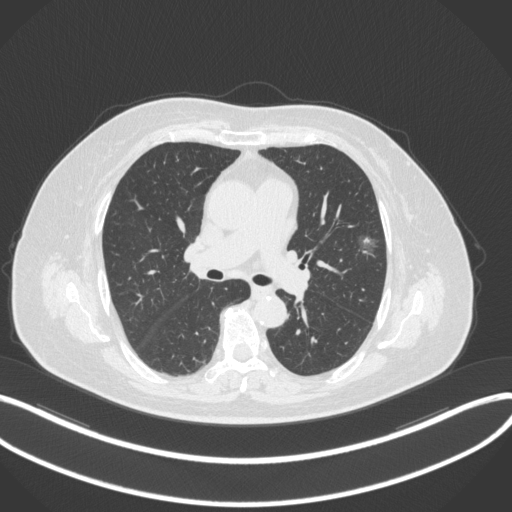
Chest CT, one axial slice; slice 184 of 286 in the series (ordered by position); reconstruction kernel B31f; 120 kVp; lung window (W 1500 / L -600 HU); 1 mm slice thickness; 512 × 512 image matrix. Patient: female, 76 years. Case-level facts recorded for this patient, not image findings: clinical TNM (as recorded): T1b N0 M0; histopathological grade: G1-2.
Structures marked on this image (bounding box drawn by a radiologist):
- lung tumour (recorded histology: adenocarcinoma): bounding box [x1, y1, x2, y2] px = [353, 227, 383, 262]